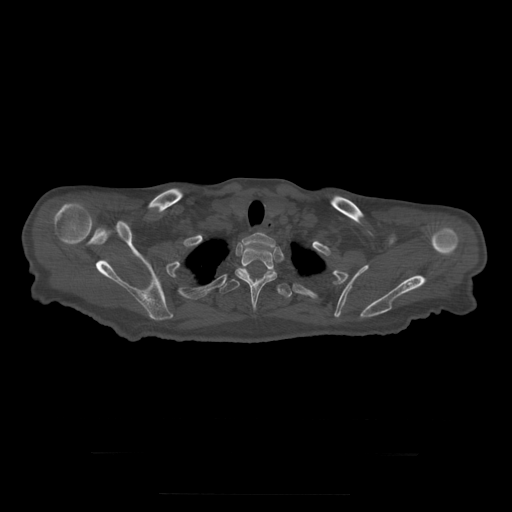
CT including the spine, one axial slice. Slice 271 of 397 in the series (ordered by position). 120 kVp. Bone window (W 1800 / L 400 HU). 1.25 mm slice thickness. 512 × 512 image matrix, field of view 510 × 510 mm. Patient age 73 years. From the clinical record (not read from this slice): primary cancer: prostate.
Outlined on this slice (semi-automatically segmented with operator editing):
- T1 vertebra: bounding box <242,231,276,248> (left, top, right, bottom; pixels)
- T2 vertebra: <235,246,277,310>
- T3 vertebra: <220,268,292,298>